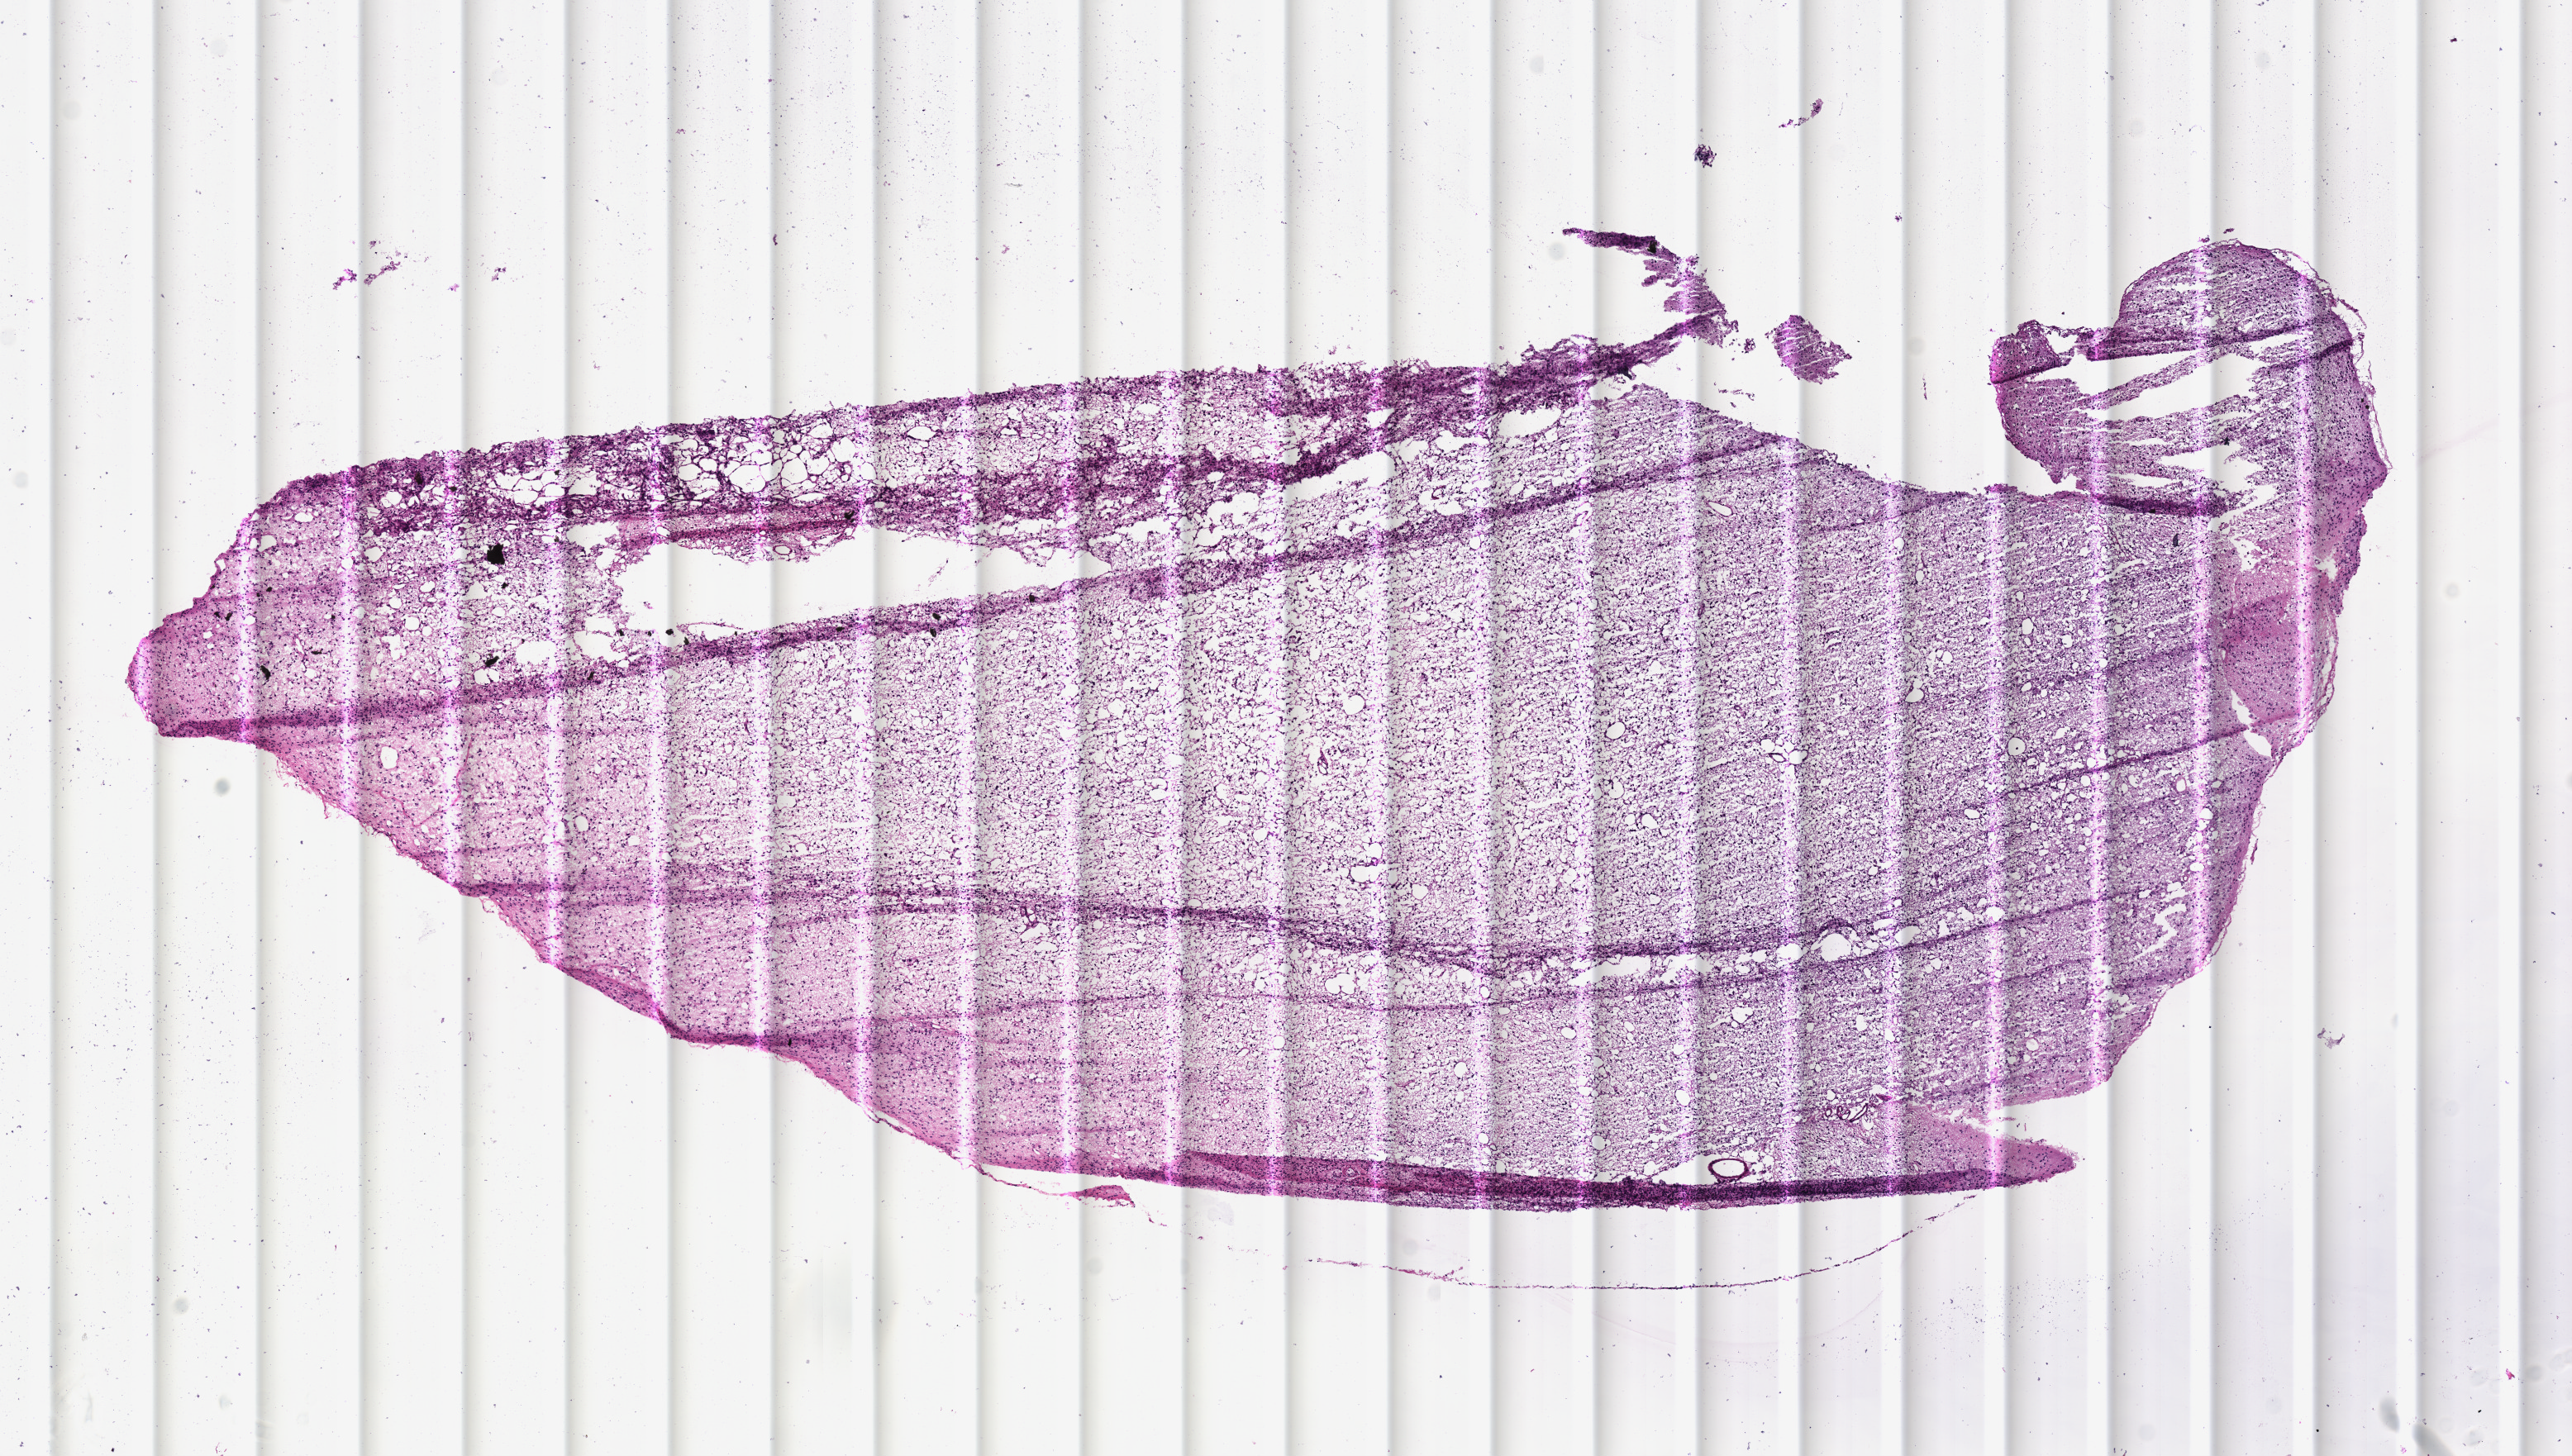
Digitized H&E tissue section (whole slide) — a low-resolution overview of the entire scanned area, about 12.2 x 6.9 mm (acquisition: 40x scan). Frozen section from the top of the tissue portion. Brain, primary tumour sample. Male, age 48 years at initial diagnosis. Histologic grade: G3 (poorly differentiated). Composition of this section per pathologist review: tumour cells 100%, tumour nuclei 70%, normal cells 0%, stromal cells 0%, necrosis 0%.
• laterality: left
• histologic diagnosis: Astrocytoma, anaplastic (cerebrum)